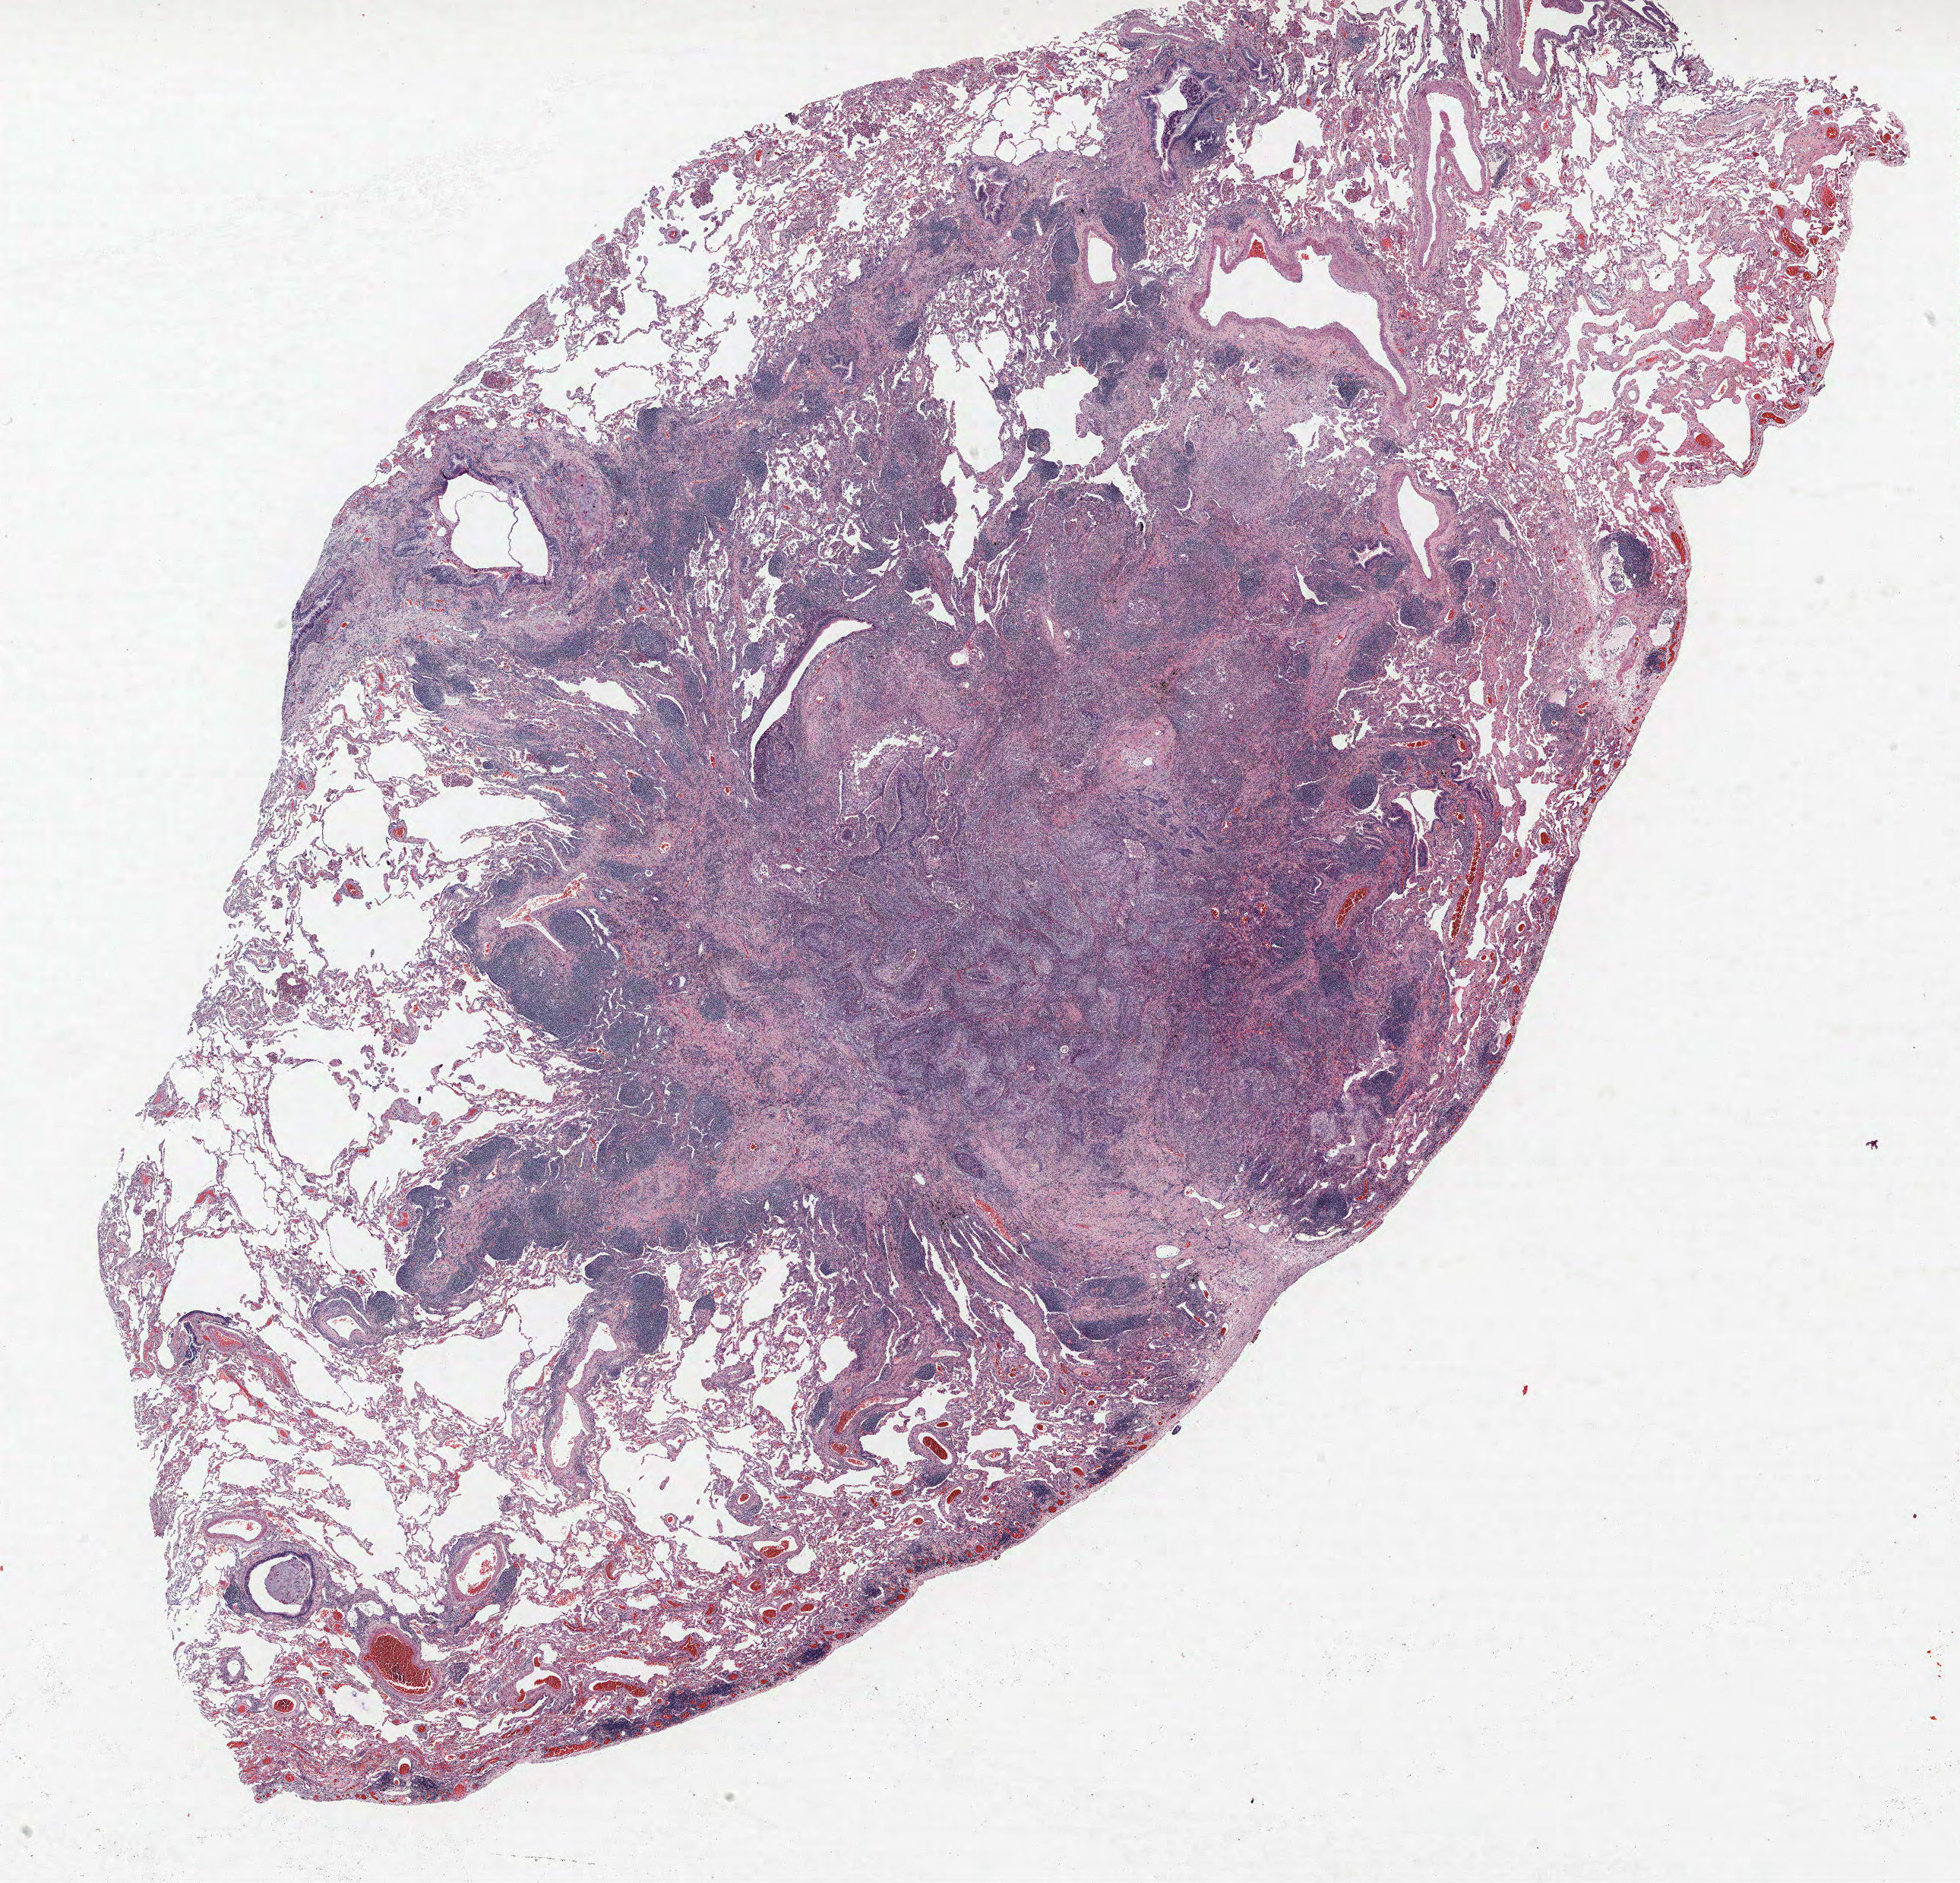
Whole-slide histology image, H&E-stained — shown as a low-resolution overview of the whole scanned area (about 20.6 x 19.8 mm, acquisition: 40x scan); formalin-fixed paraffin-embedded (FFPE) section; lung. Female, age 56 at enrolment. Grade: moderately differentiated (G2).
Tumour size (pathology): 17 mm. Primary tumour location (clinical record): right lower lobe. Participant's lung-cancer diagnosis: Squamous cell carcinoma, NOS. Stage (AJCC 6th edition): IA.